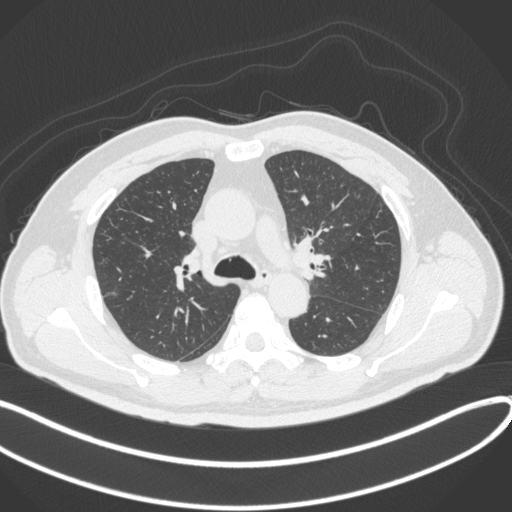
Chest CT, one axial slice. Slice 229 of 373 in the series (ordered by position). Reconstruction kernel B31f. 120 kVp. Lung window (W 1500 / L -600 HU). 1 mm slice thickness. 512 × 512 image matrix, field of view 400 × 400 mm. Male patient, age 60 years. Case-level facts recorded for this patient, not image findings: clinical TNM (as recorded): T1c N0 M0.
Structures marked on this image (bounding box drawn by a radiologist):
- lung tumour (recorded histology: adenocarcinoma): bounding box <103,287,124,302> (left, top, right, bottom; pixels)